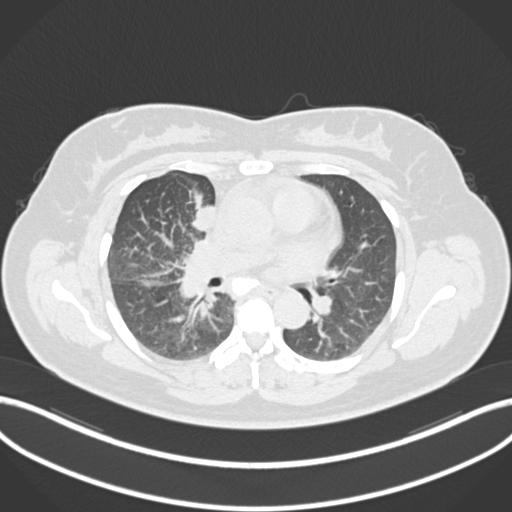
Chest CT, one axial slice; slice 93 of 183 in the series (ordered by position); 120 kVp; lung window (W 1500 / L -600 HU); 512 × 512 image matrix, field of view 400 × 400 mm. Female patient, age 46 years. Case-level facts recorded for this patient, not image findings: clinical TNM (as recorded): T2a N1 M0.
Structures marked on this image (bounding box drawn by a radiologist):
- lung tumour (recorded histology: adenocarcinoma): bounding box (x1, y1, x2, y2) in pixels: (187, 193, 218, 236)